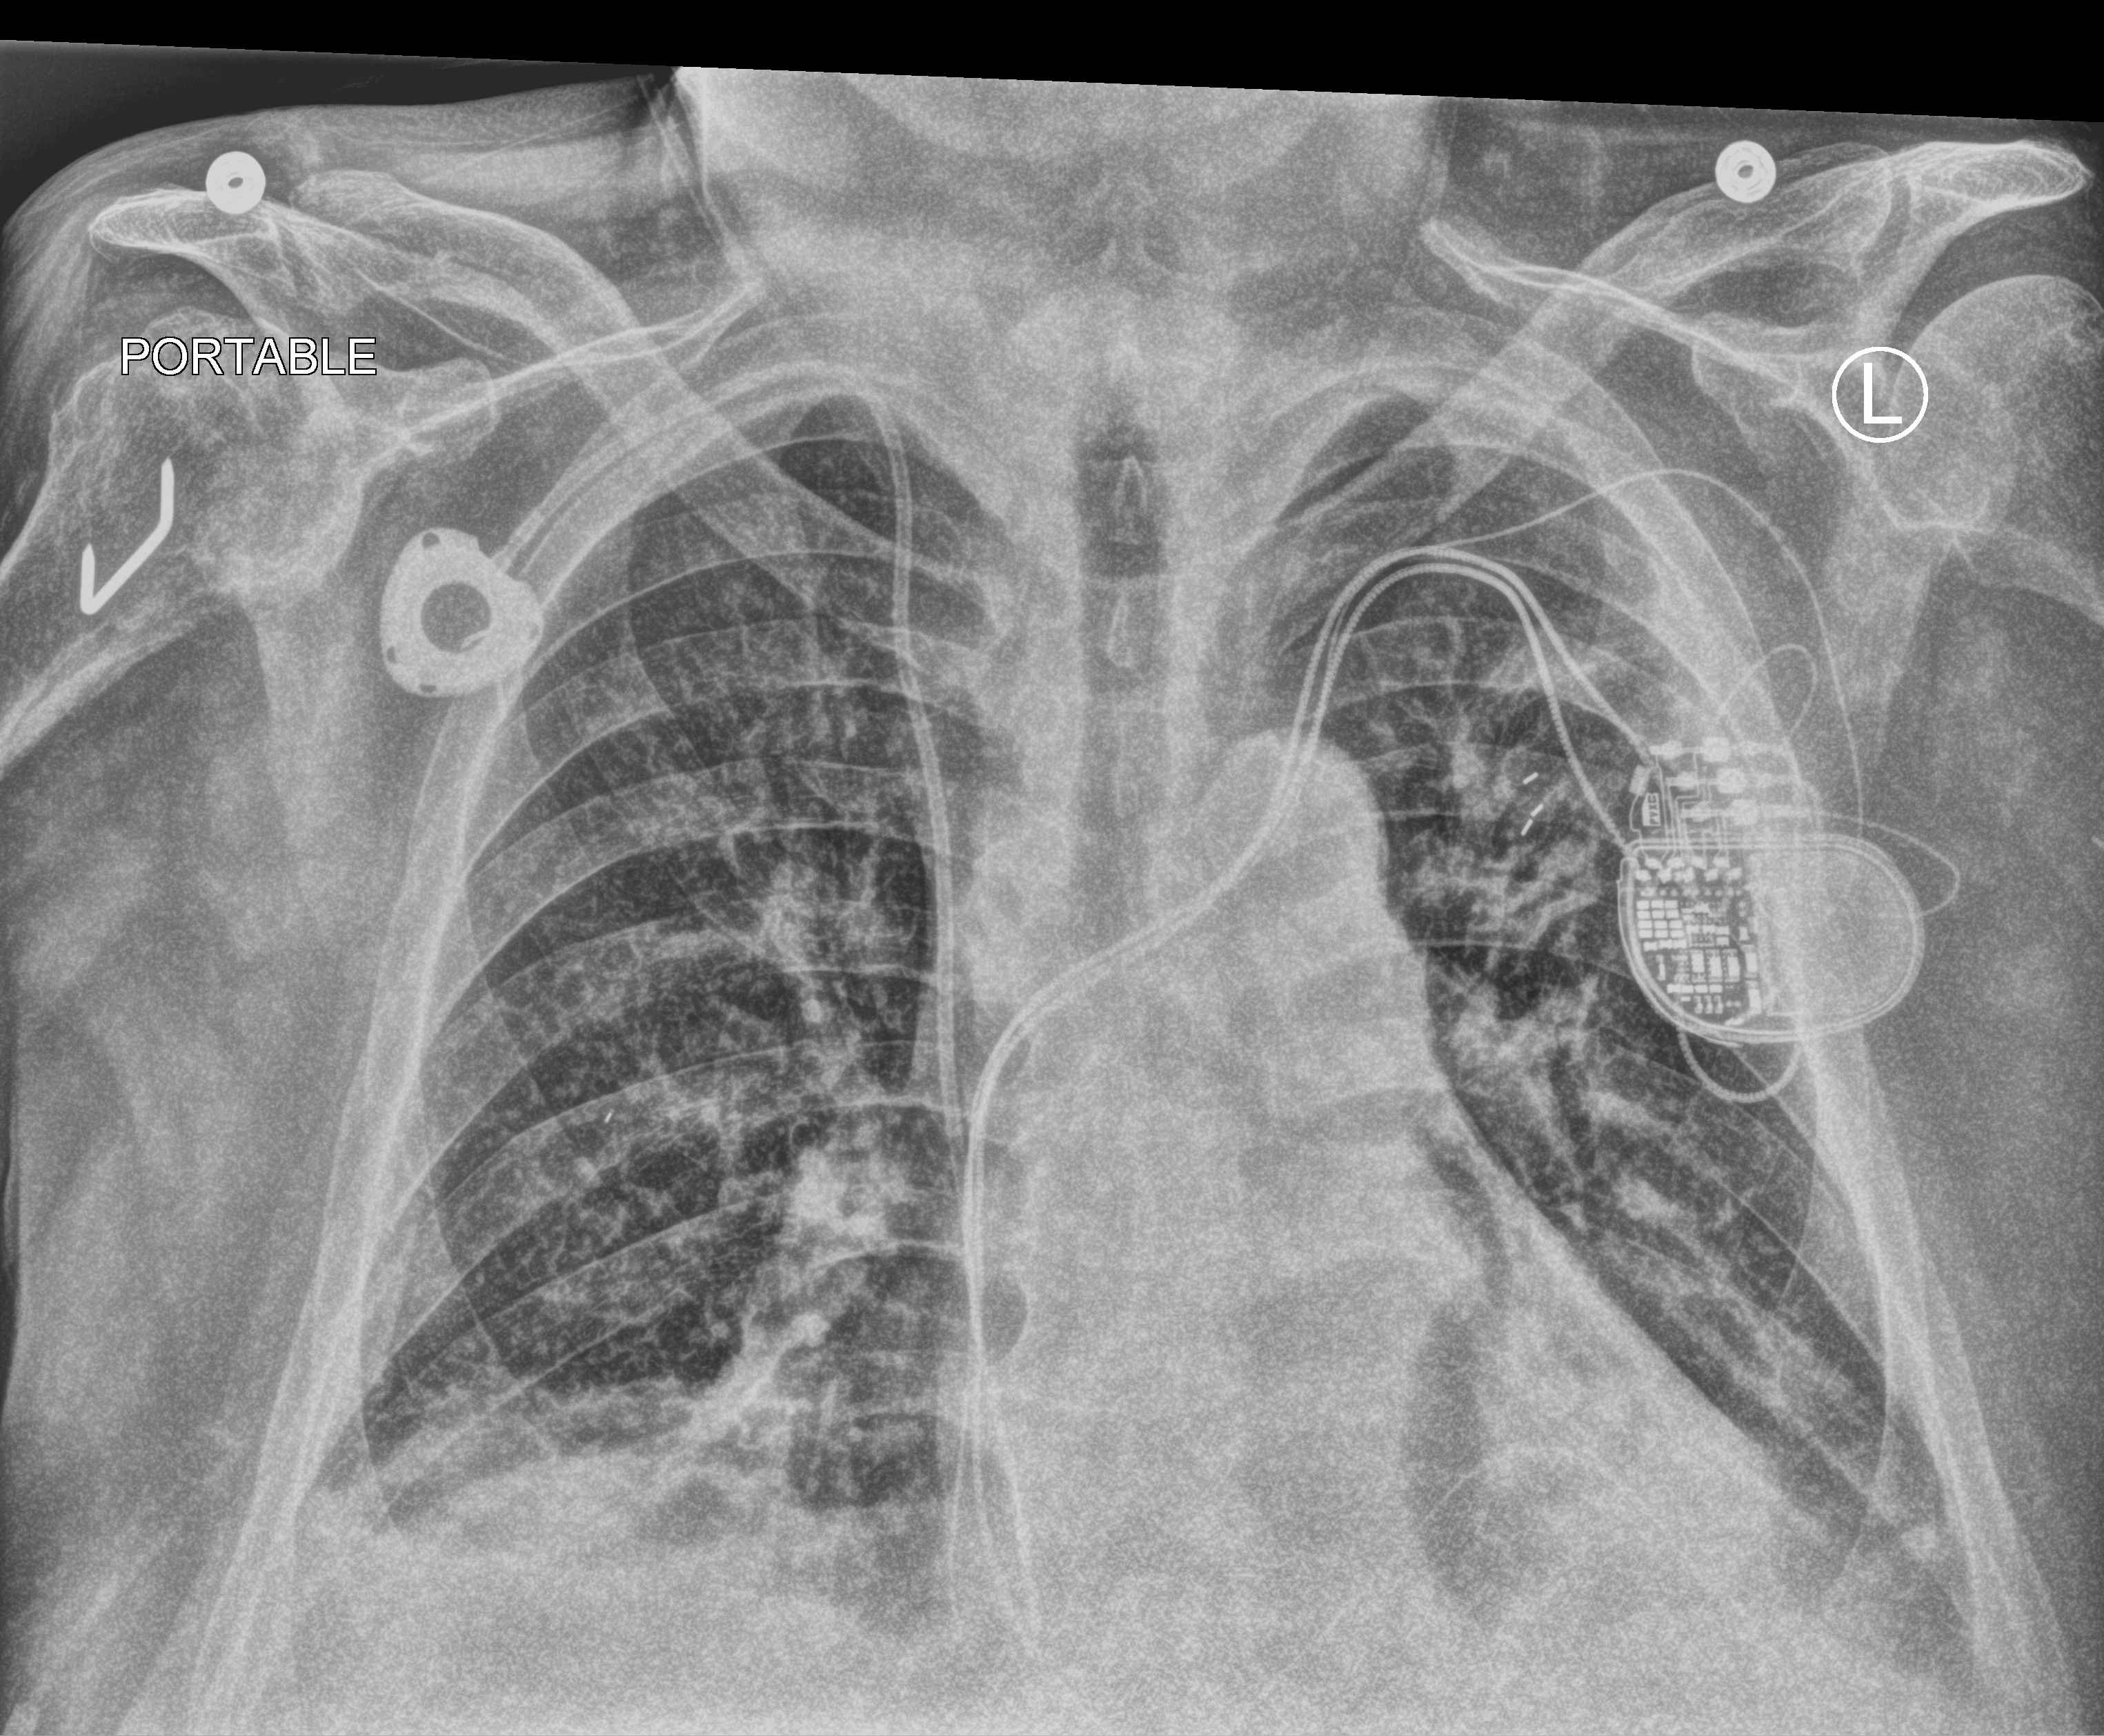
Portable chest radiograph, anteroposterior (AP) projection. Male patient hospitalised with COVID-19, age 60–74 years.
Hospital-stay facts (about this admission, not read from this image; timing relative to this image not recorded):
- mechanically ventilated during this hospital stay: no
- admitted to intensive care during this hospital stay: yes
- length of hospital stay: 20 days